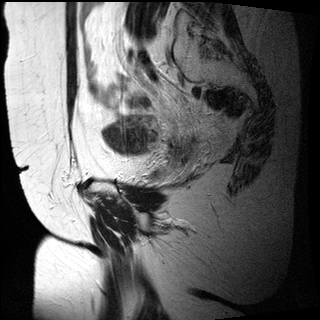
Pelvic MRI for cervical cancer, one sagittal slice. Position 21 of 27 along the scan axis. T2-weighted. 1.5 T. TE 89 ms, TR 2740 ms. 4 mm slice thickness. 320 × 320 image matrix, field of view 260 × 260 mm. Female patient, age 47 years.
Annotated regions visible in this slice (manually delineated by an expert):
- uterus and cervix: bounding box <102,118,155,155> (left, top, right, bottom; pixels)